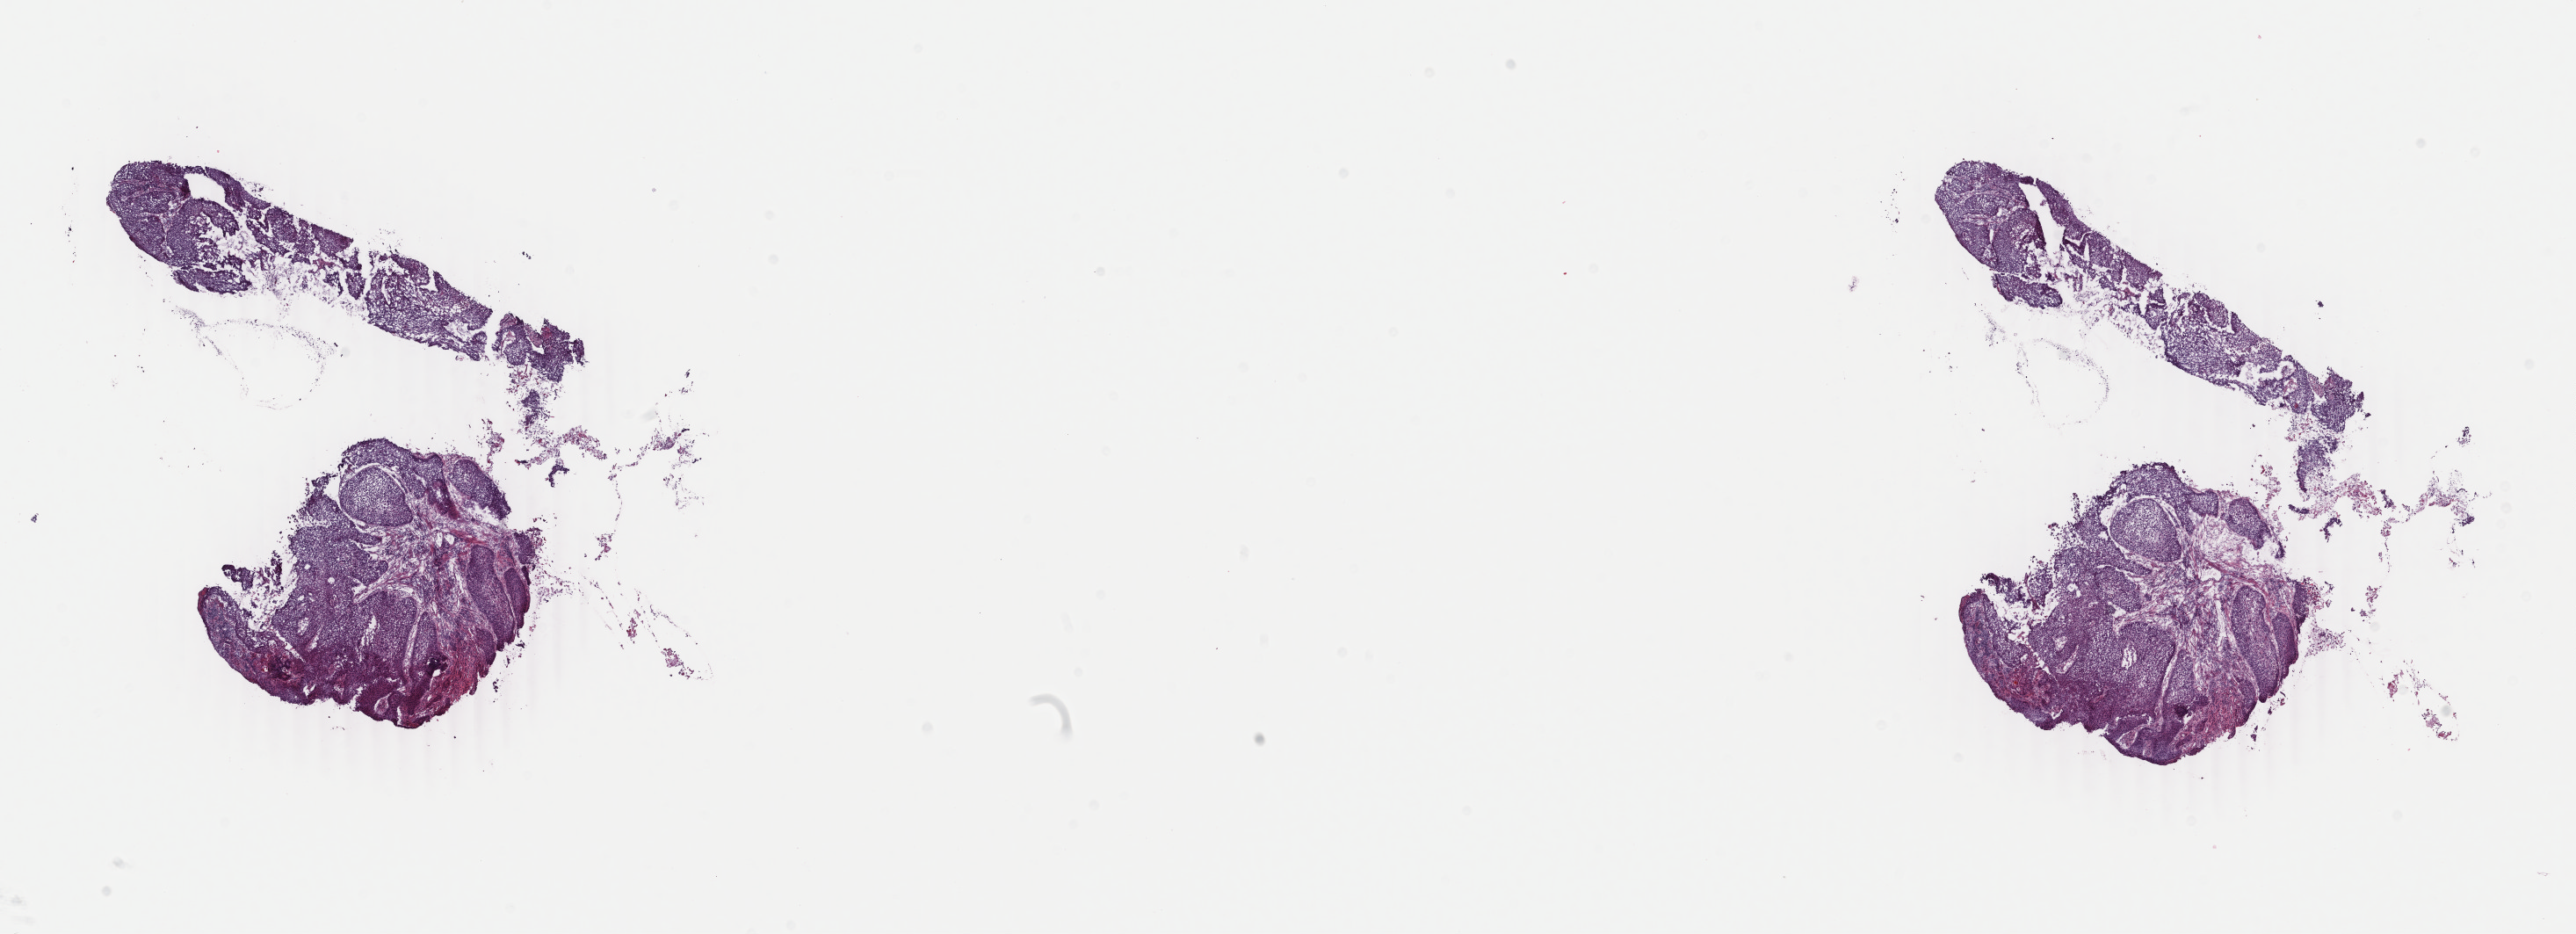
Whole-slide histology image, H&E, shown as a low-resolution overview of the whole scanned area (about 23.3 x 8.5 mm, from a 40x scan), frozen section, esophagus, primary tumour sample. Male patient; age at initial diagnosis 51 years.
Diagnosis: Squamous cell carcinoma, NOS.